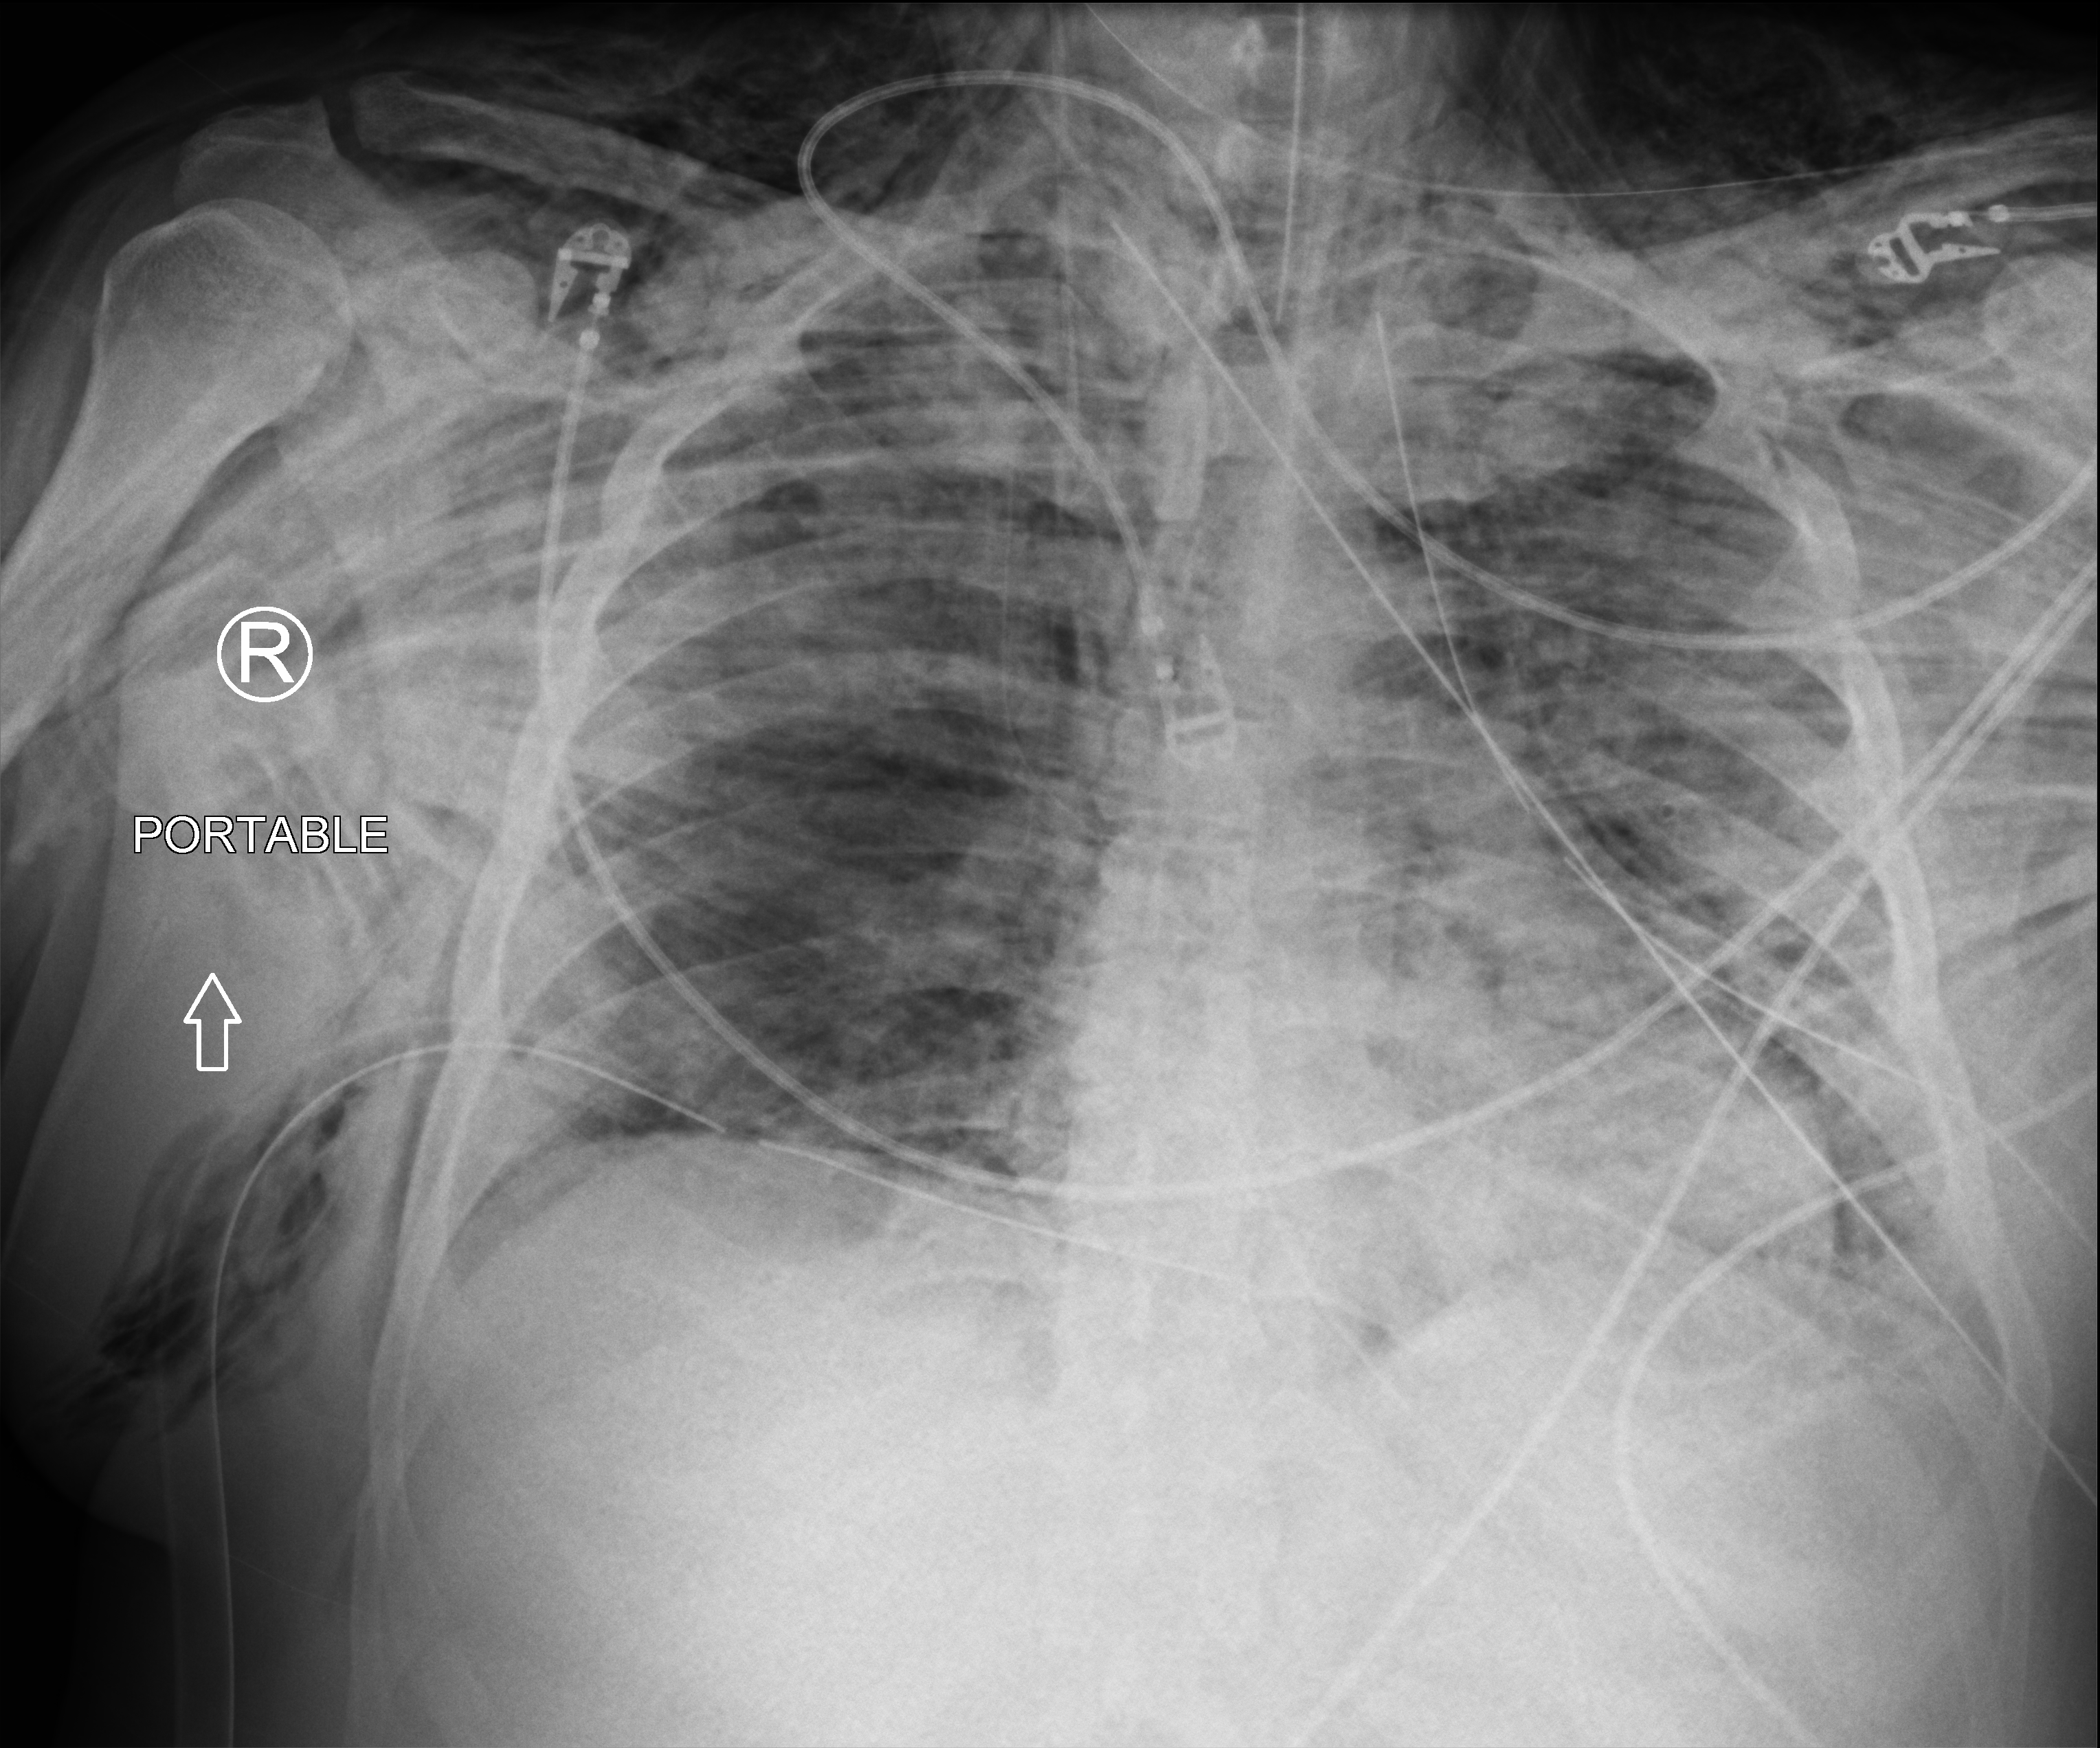
Chest X-ray (portable), anteroposterior (AP) projection. Patient hospitalised with COVID-19; male, aged 18–59 years.
Hospital-stay facts (about this admission, not read from this image; timing relative to this image not recorded): admitted to intensive care during this hospital stay: yes; mechanically ventilated during this hospital stay: yes.